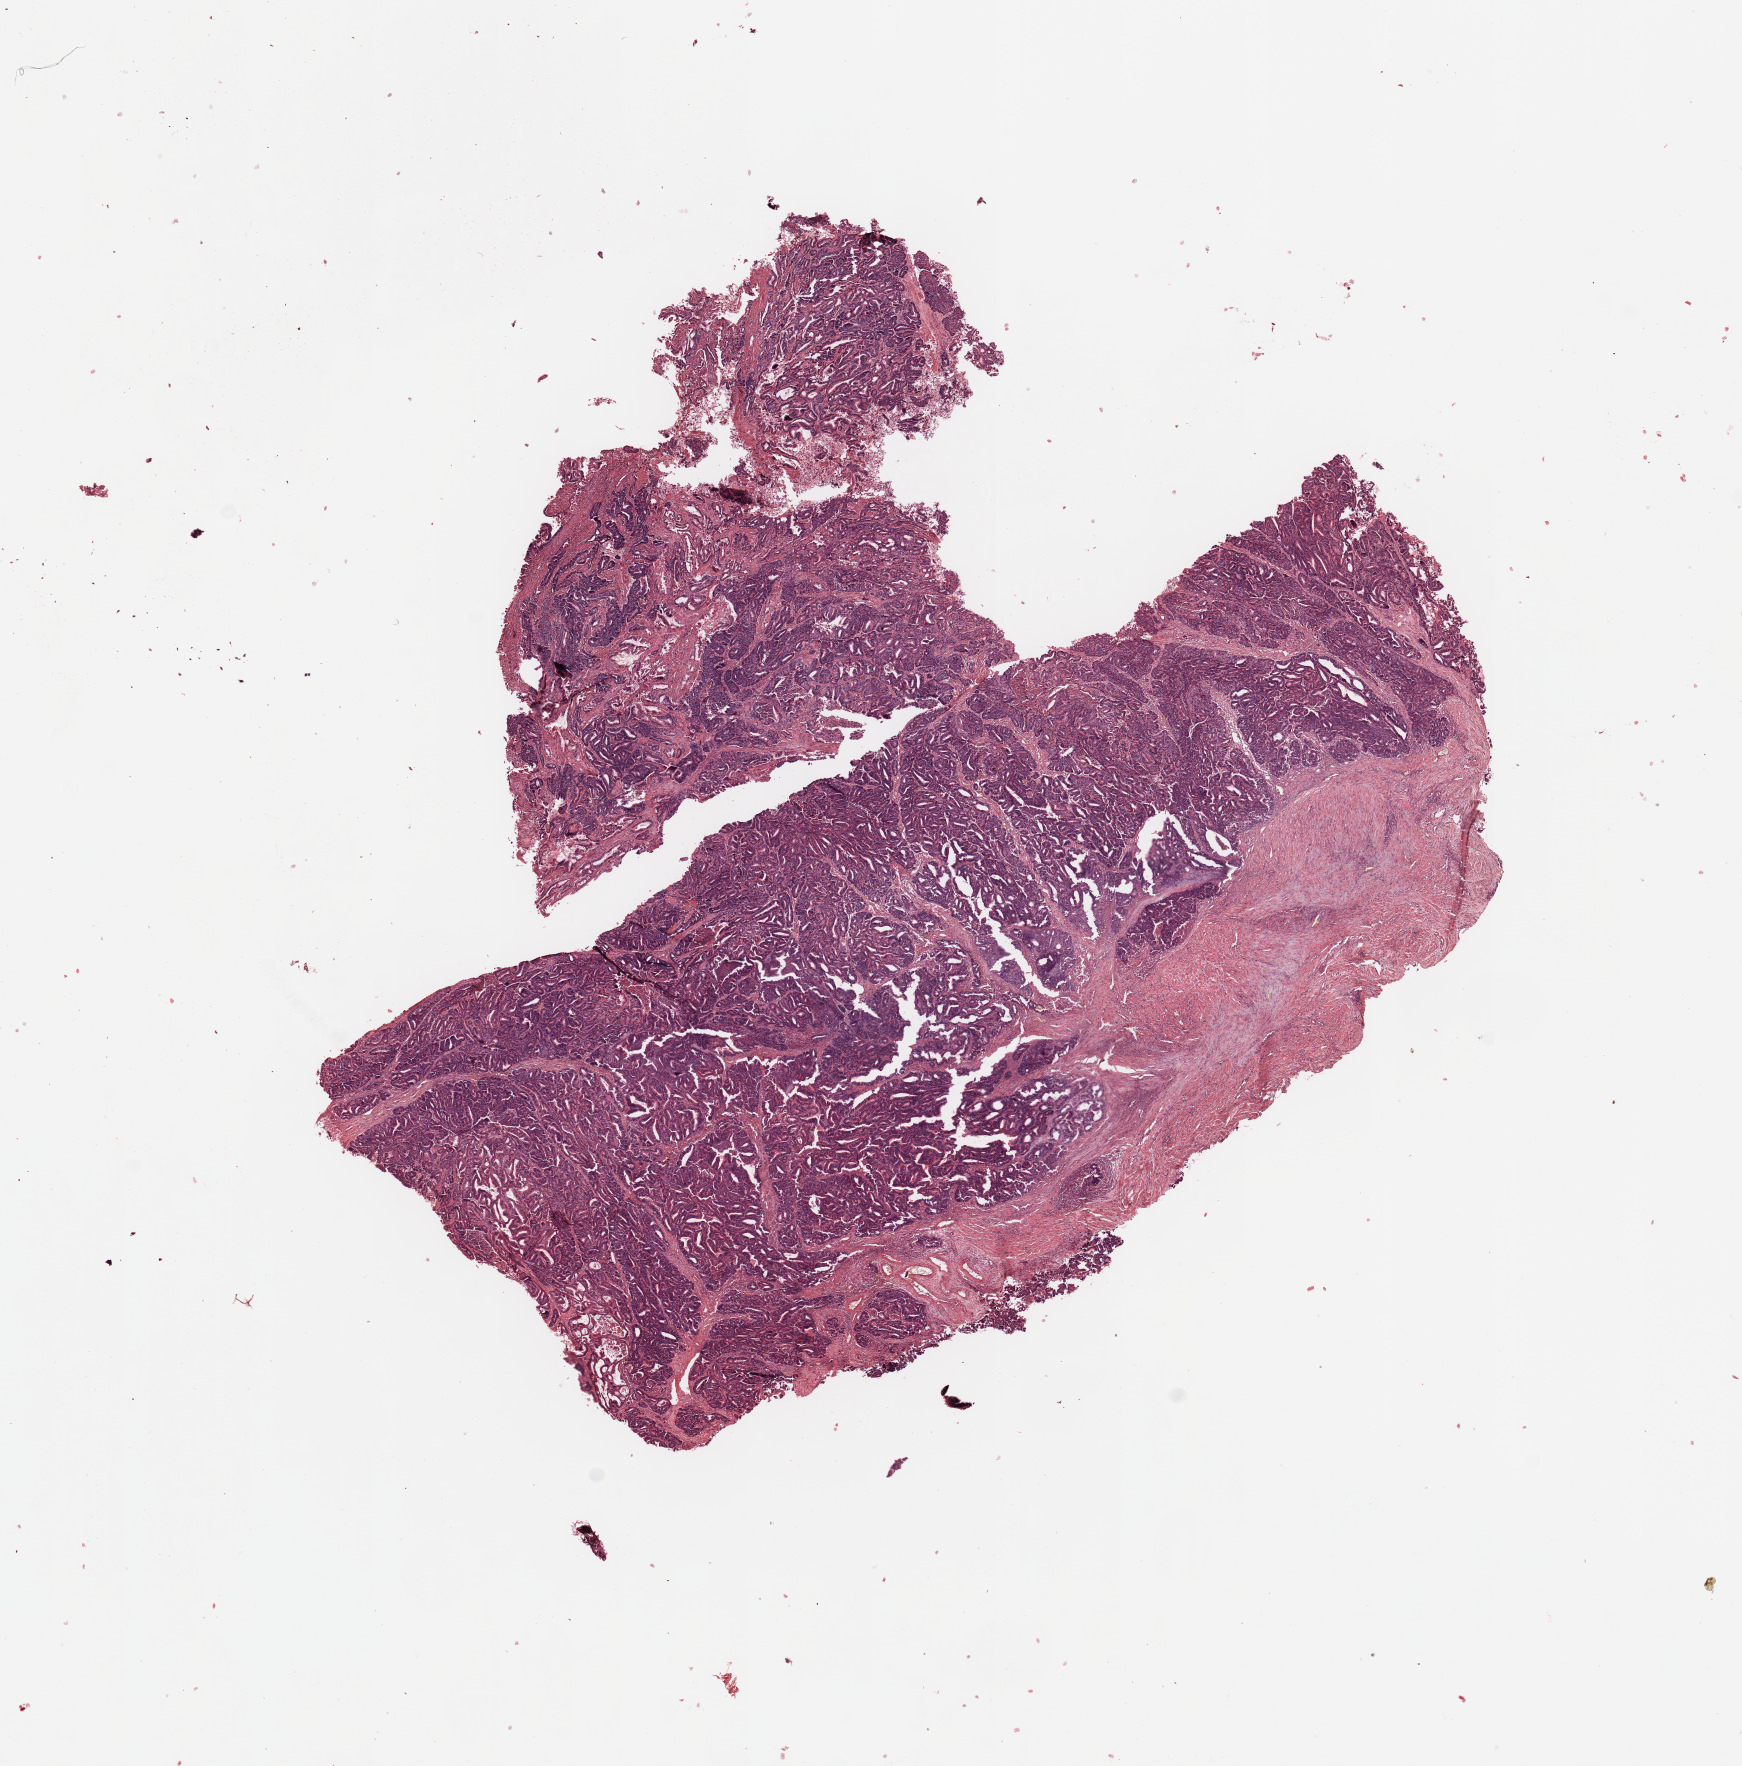
Digitized Hematoxylin and eosin (H&E) stained tissue section (whole slide), whole scanned area (about 13.8 x 14.0 mm, from a 20x scan) shown as a low-resolution overview, uterus, tumour tissue. Patient: female, age 68 years. Histologic grade: G2 (moderately differentiated).
* AJCC pathologic stage: III
* histologic diagnosis: Endometrioid adenocarcinoma, NOS